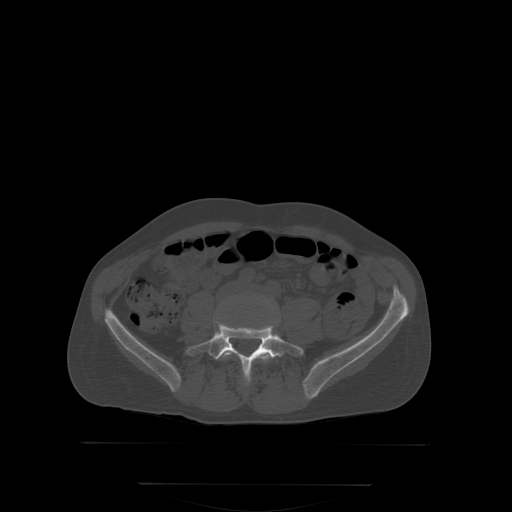
CT including the spine, one axial slice; slice 99 of 350 in the series (ordered by position); bone window (W 1800 / L 400 HU); 2.5 mm slice thickness; 512 × 512 image matrix, field of view 500 × 500 mm. Patient: male, 58 years. Case-level facts recorded for this patient, not image findings: primary cancer: prostate.
Structures marked on this image (semi-automatic segmentation, software-assisted and operator-edited):
- L4 vertebra: bounding box (x1, y1, x2, y2) in pixels: (221, 298, 272, 362)
- L5 vertebra: (187, 322, 304, 386)